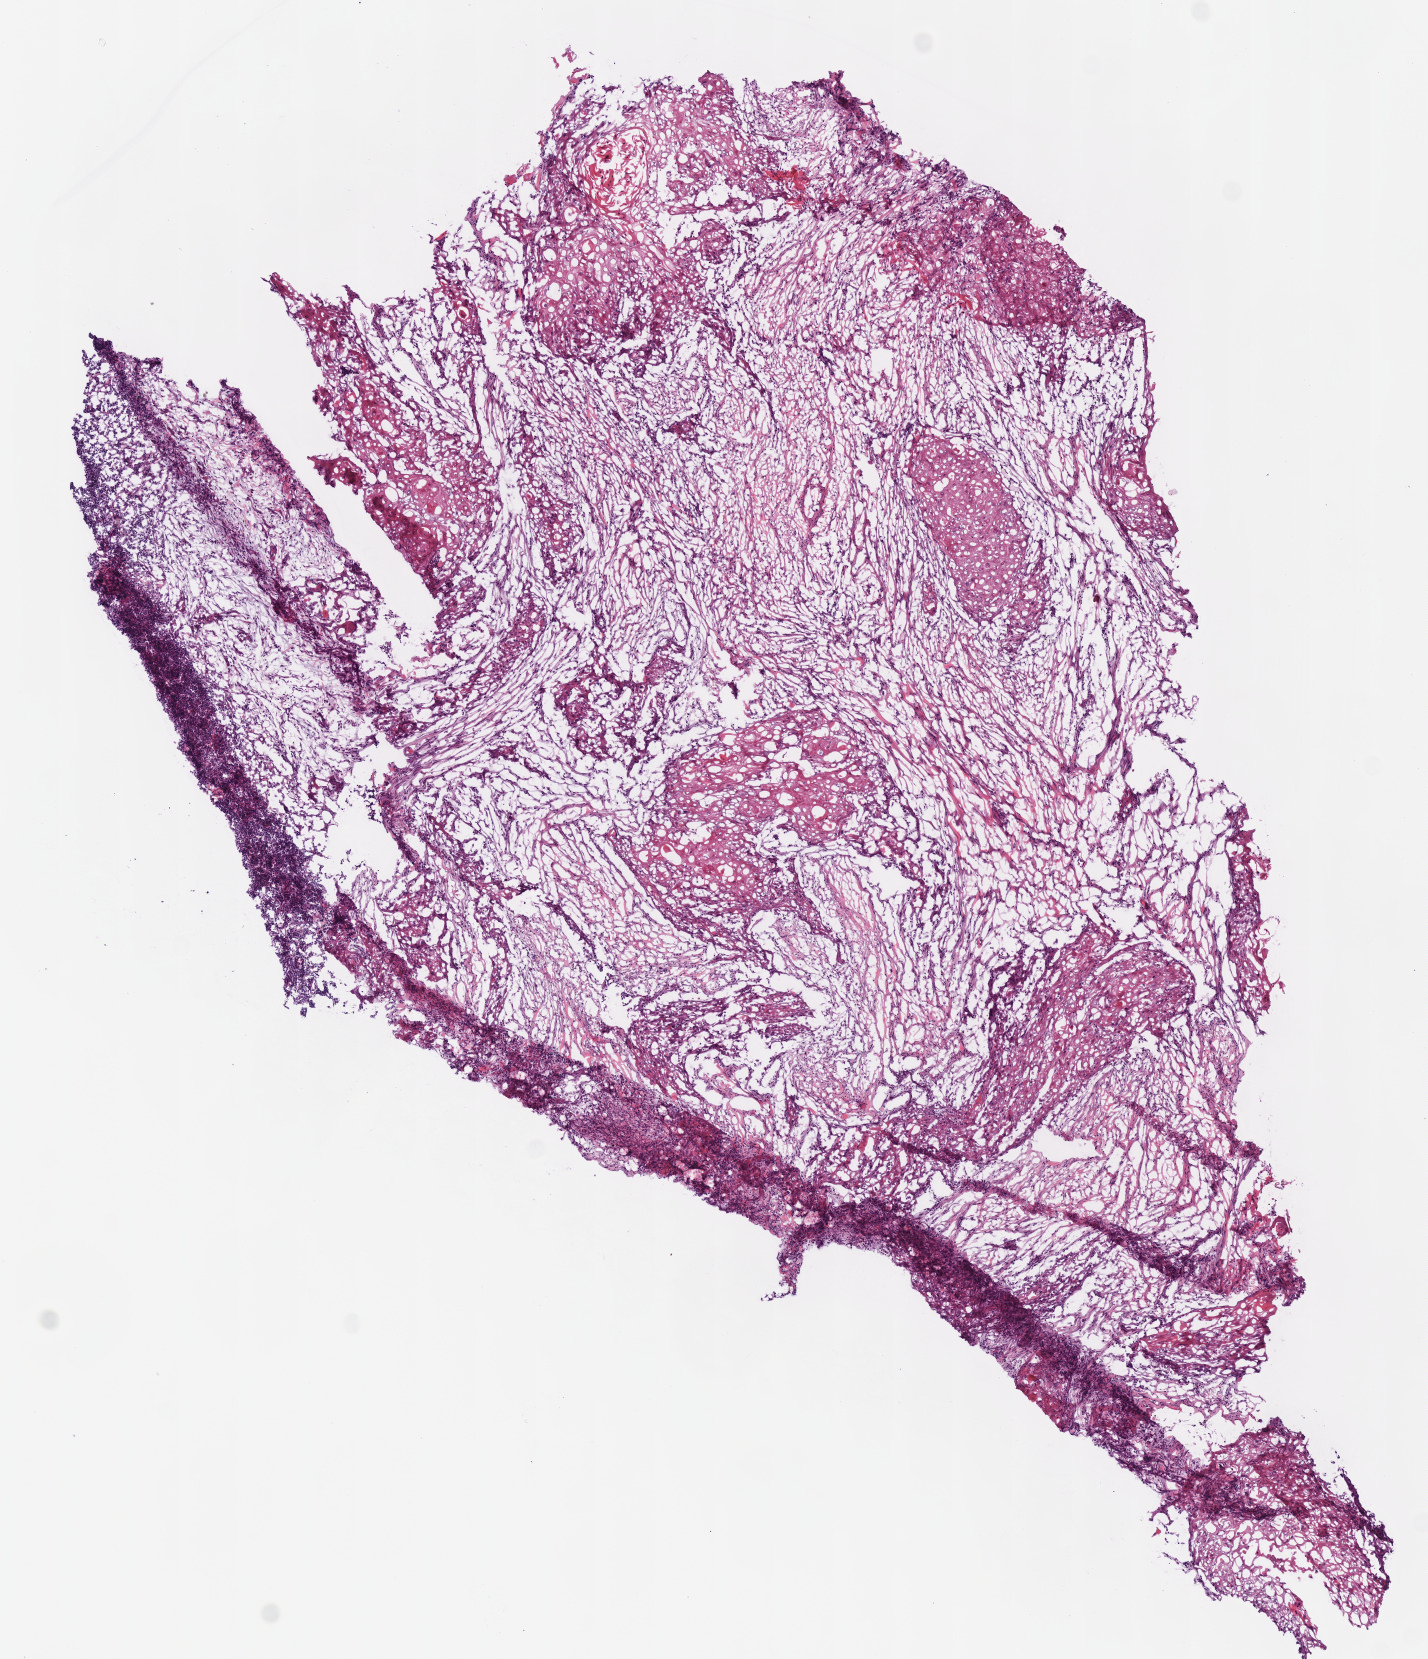
Whole-slide histology image, Hematoxylin and eosin (H&E) stained — a low-resolution overview of the entire scanned area, about 5.6 x 6.5 mm (acquisition: 40x scan). Frozen section. Sample: primary tumour, head and neck. Patient: male, age at initial diagnosis 61 years.
Histologic diagnosis: Squamous cell carcinoma, NOS.